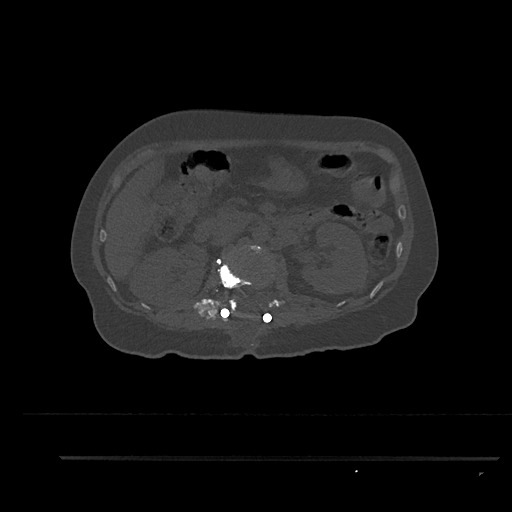
CT including the spine, one axial slice. Slice 194 of 797 in the series (ordered by position). Reconstruction kernel Br40s/3. 120 kVp. Bone window (W 1800 / L 400 HU). 512 × 512 image matrix. Female patient, age 44 years. From the clinical record (not read from this slice): primary cancer: renal.
Structures marked on this image (semi-automatically segmented with operator editing):
- L1 vertebra: box from (x=218, y=257) to (x=253, y=317) px
- L2 vertebra: (x=225, y=245)–(x=266, y=311)